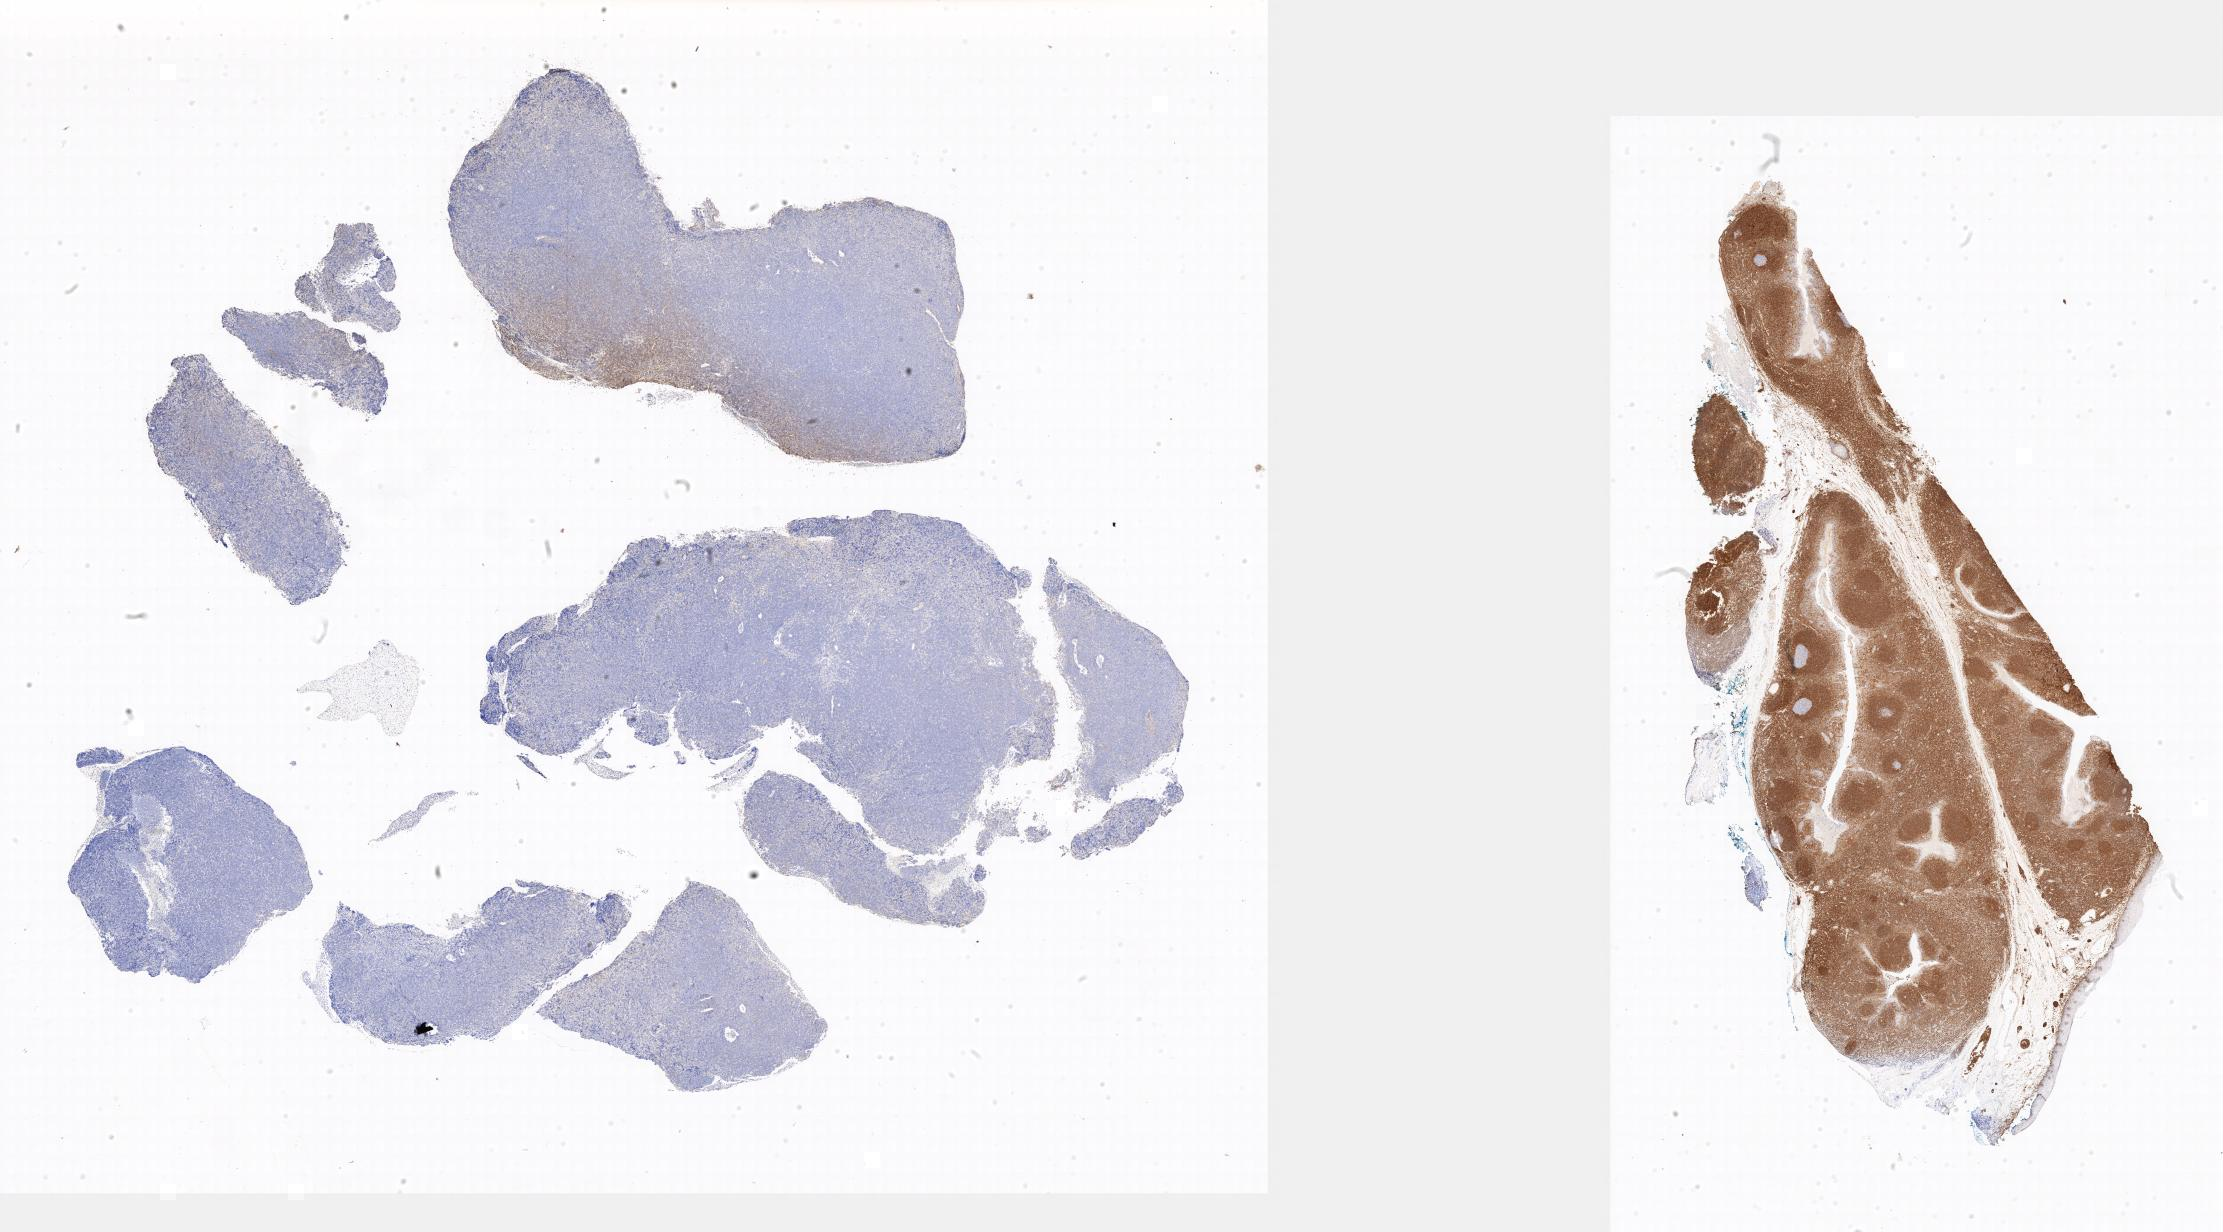
Immunohistochemistry (IHC) whole-slide image stained for BCL2 — whole scanned area shown as a low-resolution overview, tumor tissue, anatomic site: soft tissue. Female patient; age at initial diagnosis 9 years.
- histologic diagnosis: Burkitt lymphoma, NOS